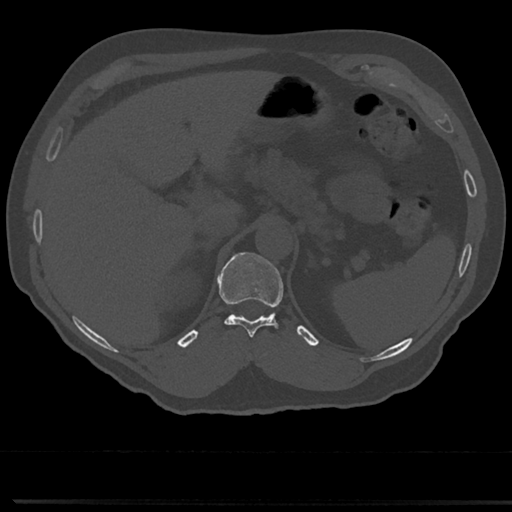
CT including the spine, one axial slice; slice 197 of 817 in the series (ordered by position); reconstruction kernel Br40s/3; 120 kVp; bone window (W 1800 / L 400 HU); 0.5 mm slice thickness; 512 × 512 image matrix, field of view 355 × 355 mm. Patient: male, 61 years. From the clinical record (not read from this slice): primary cancer: prostate.
Structures marked on this image (semi-automatically segmented with operator editing):
- T11 vertebra: bounding box (x1, y1, x2, y2) in pixels: (219, 253, 284, 339)
- T12 vertebra: (218, 252, 255, 278)